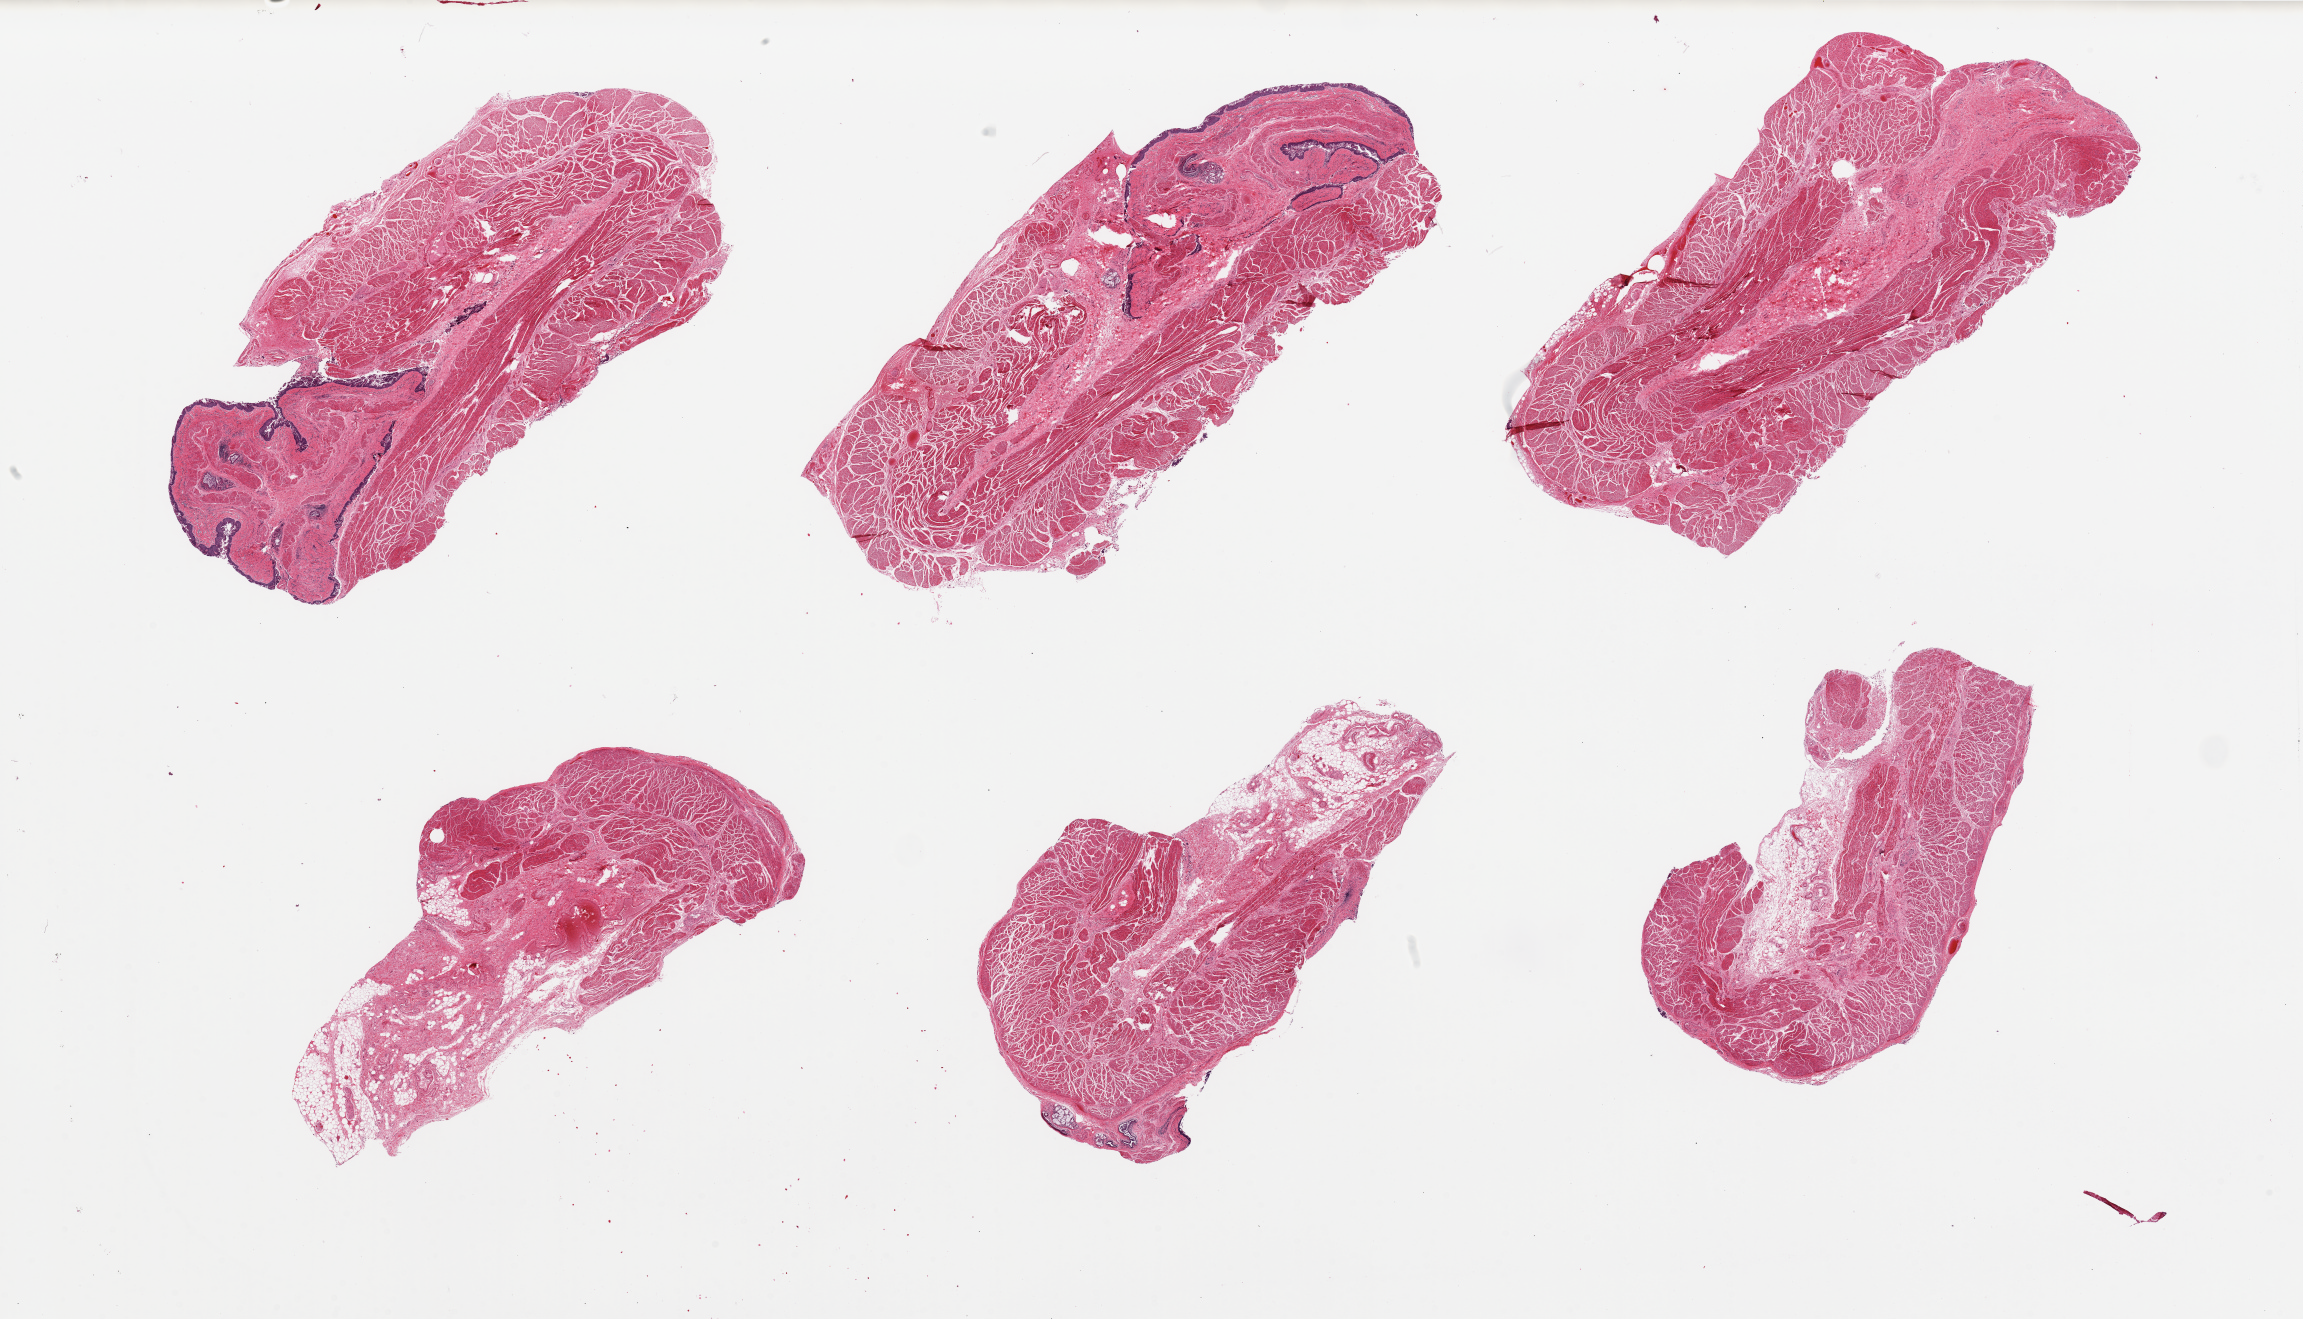
Whole-slide image, H&E stain — low-resolution overview of the scanned area, about 36.4 x 20.9 mm (slide scanned at 20x); PAXgene-fixed paraffin-embedded (PFPE) section; sampled site (target tissue): gastroesophageal junction; donor tissue sample. Female donor.
Pathologist's review note for this sample: 6 pieces, only trace mucosa/serosa attached.